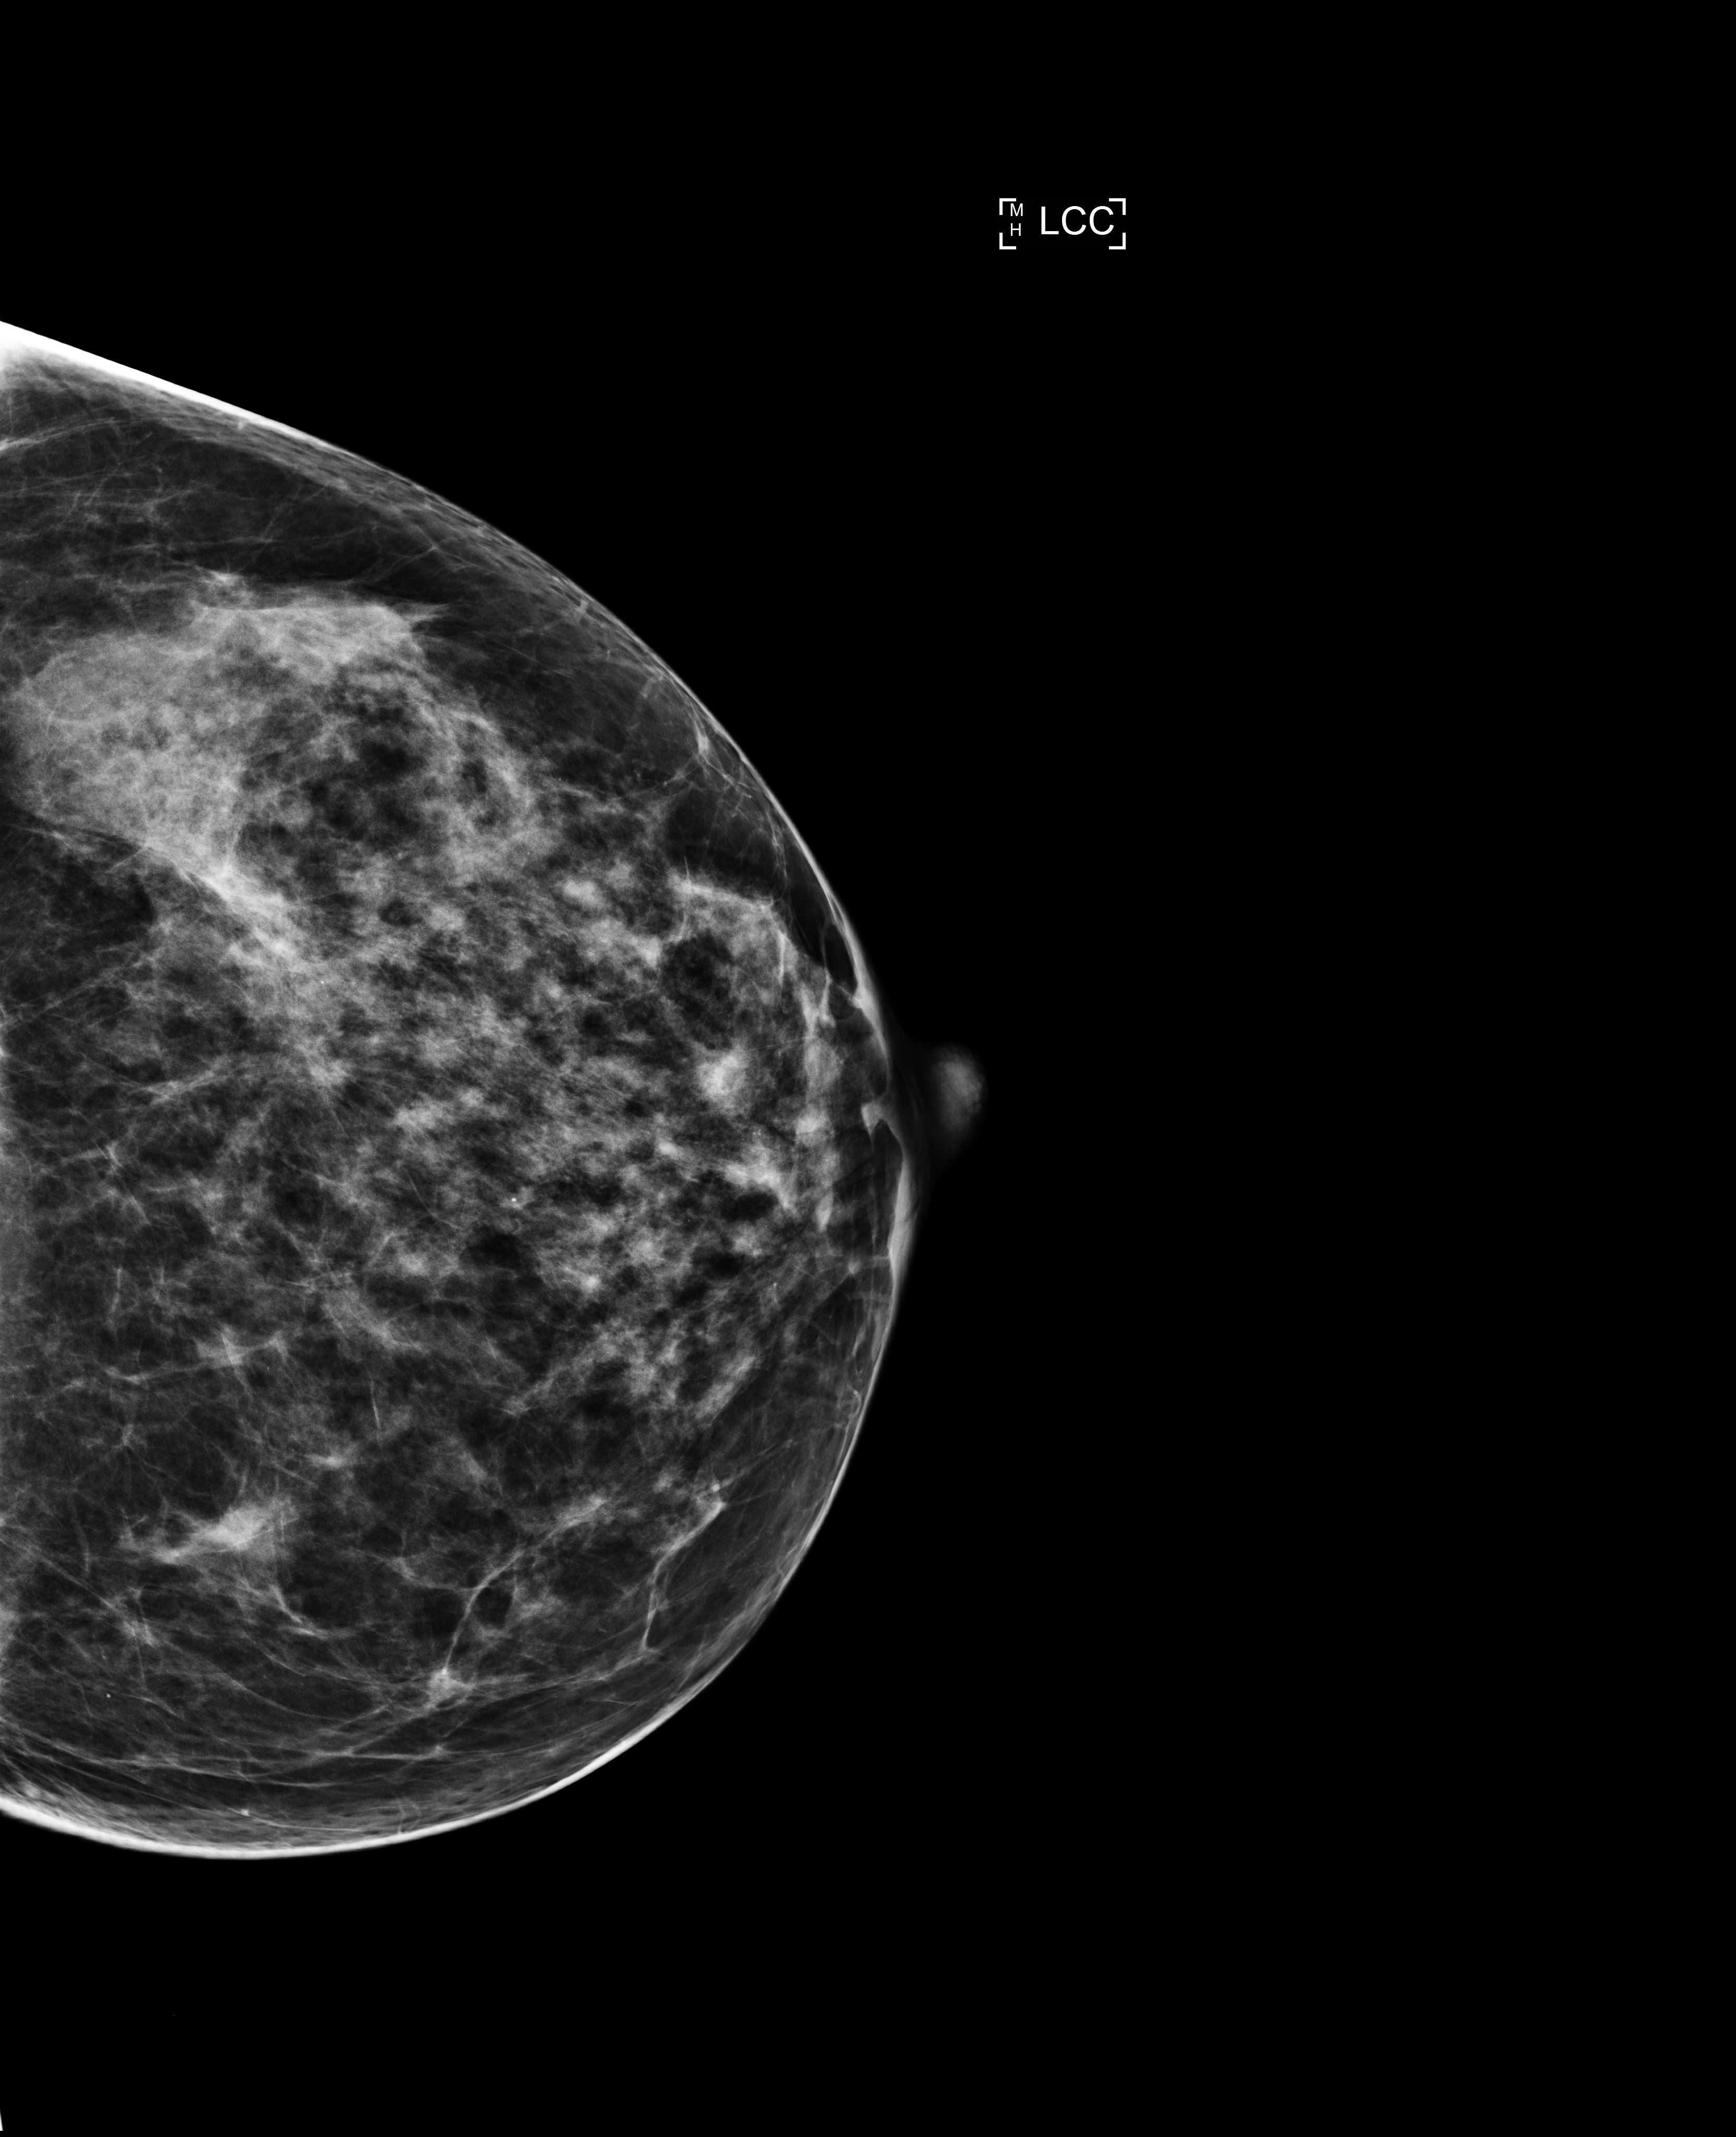
Screening examination; compressed breast thickness 71 mm. Female patient, age 48 years.
Image type: full-field digital mammogram. Breast: left. Projection: cranio-caudal projection.